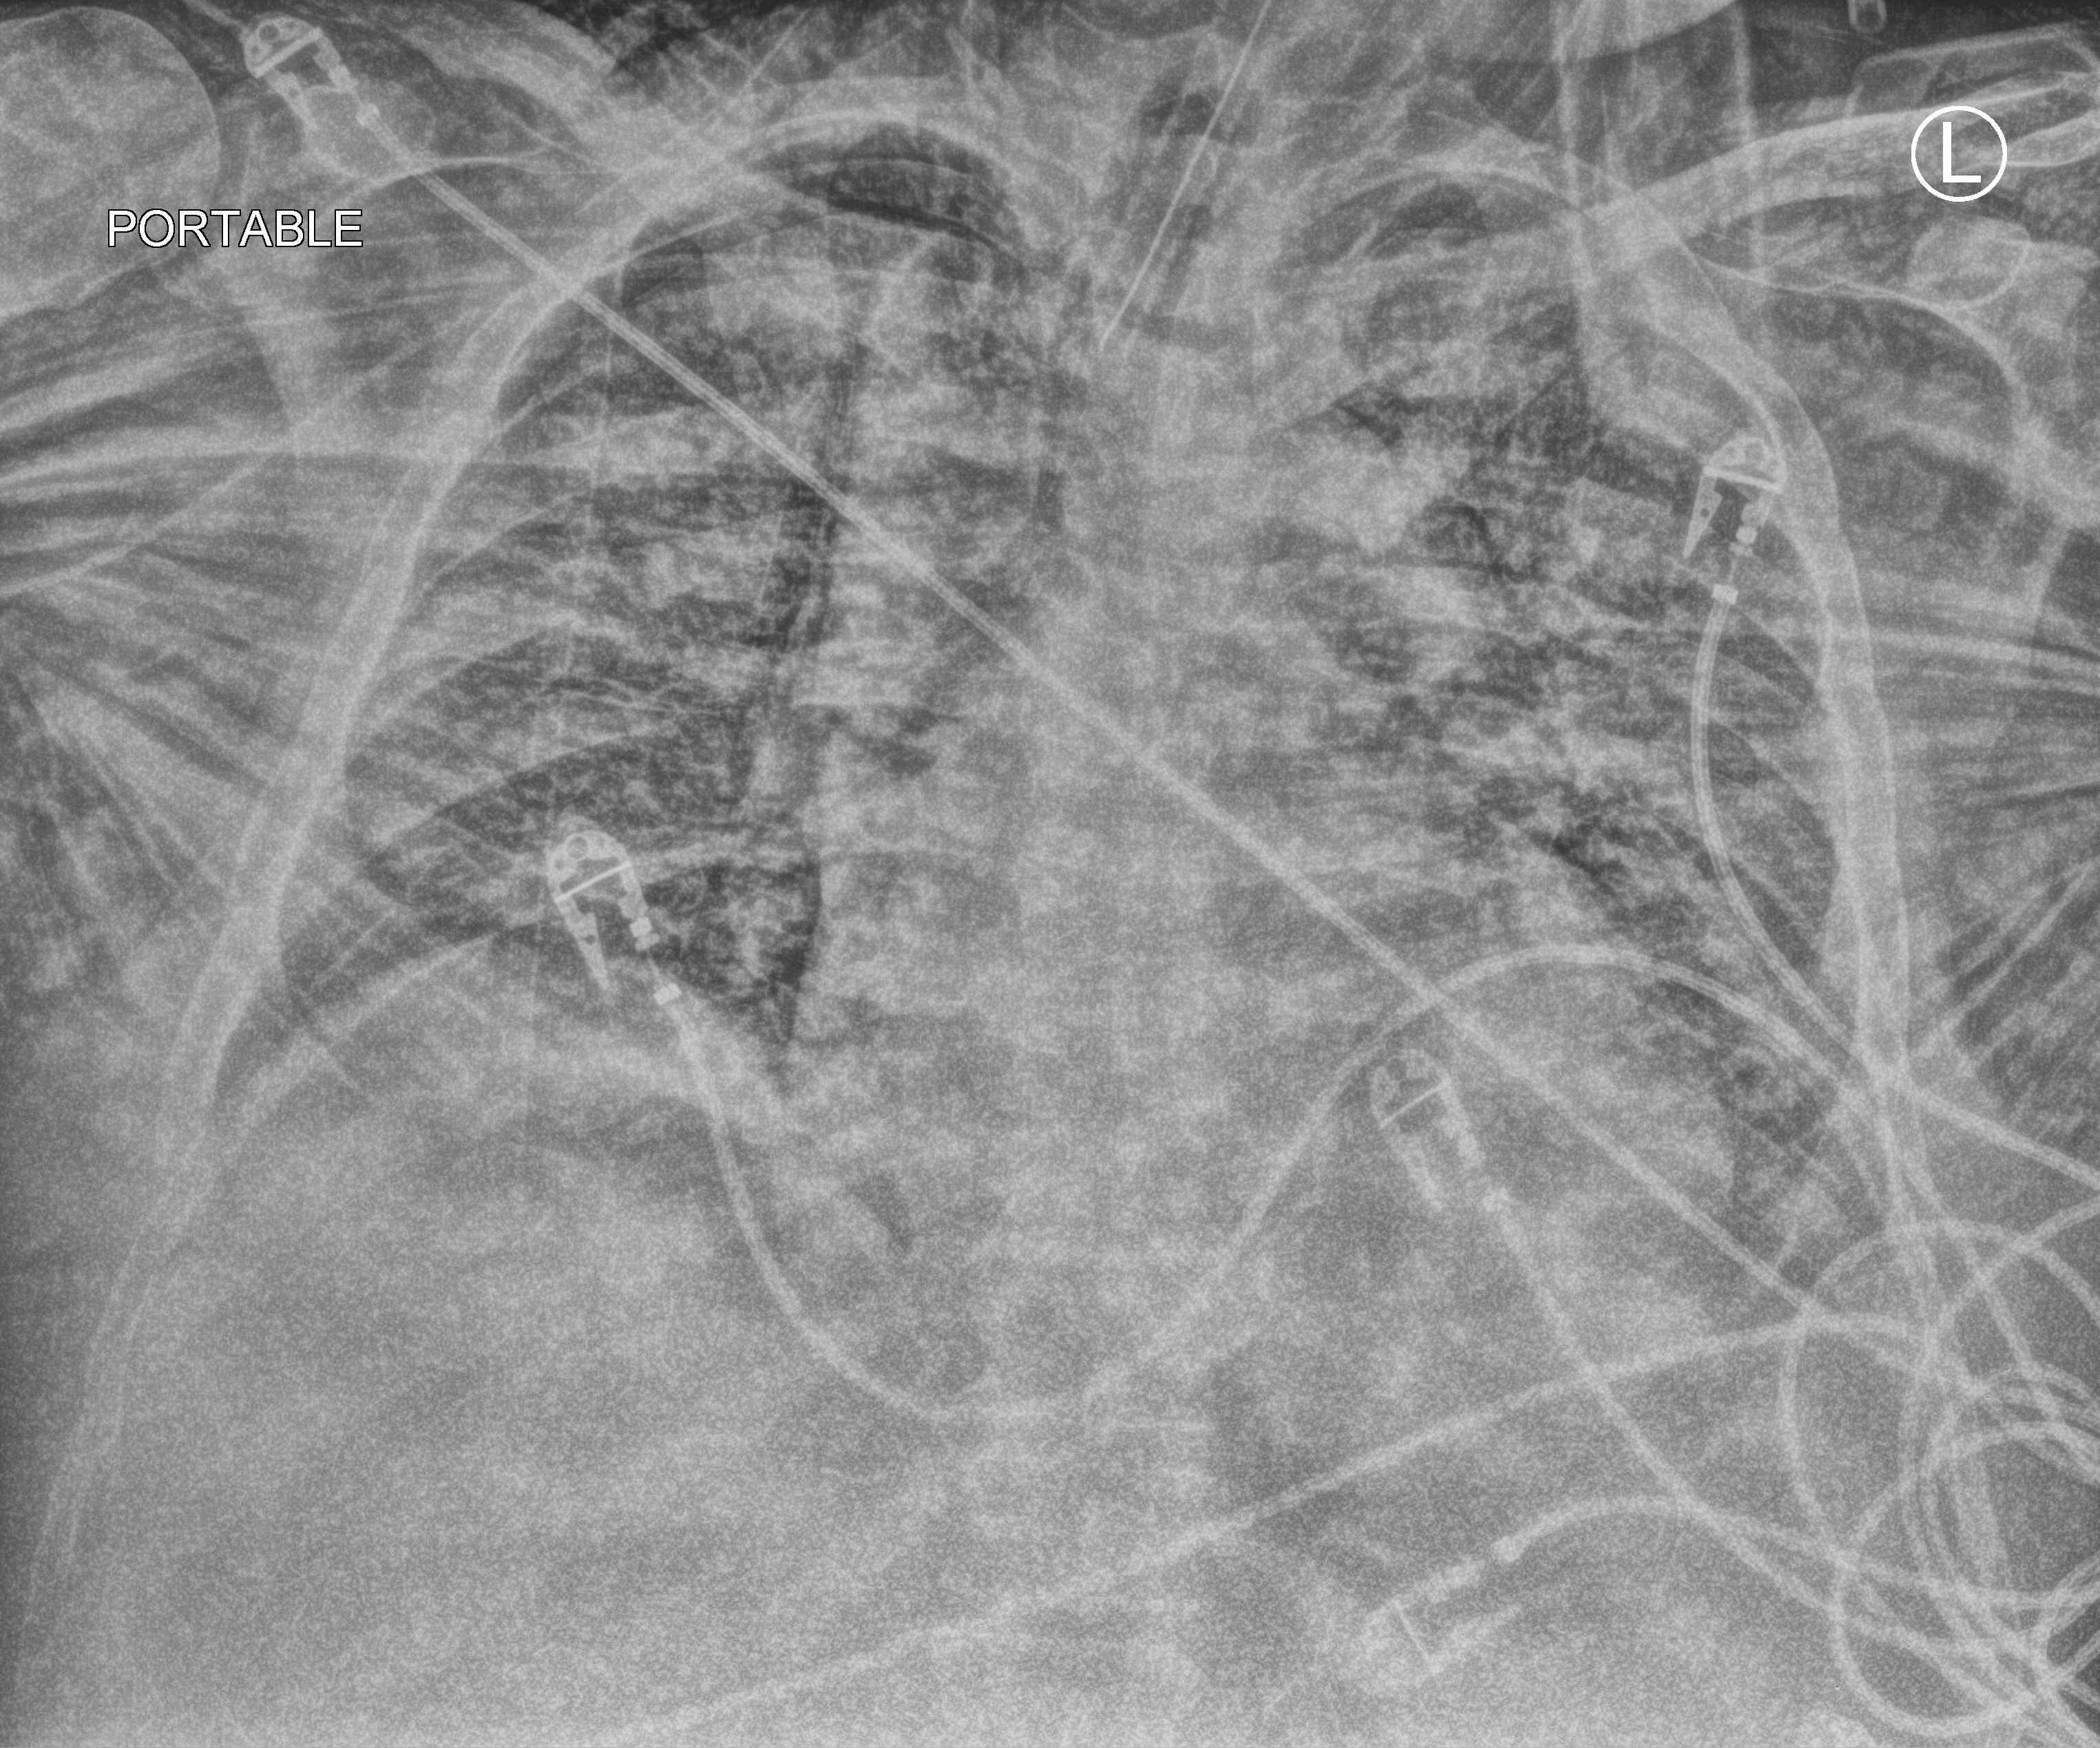
Chest X-ray (portable); anteroposterior (AP) projection. Patient hospitalised with COVID-19, aged 18–59 years.
From the hospital-stay record, not from the radiograph (when in the stay this image was taken is not recorded):
- mechanically ventilated during this hospital stay: yes